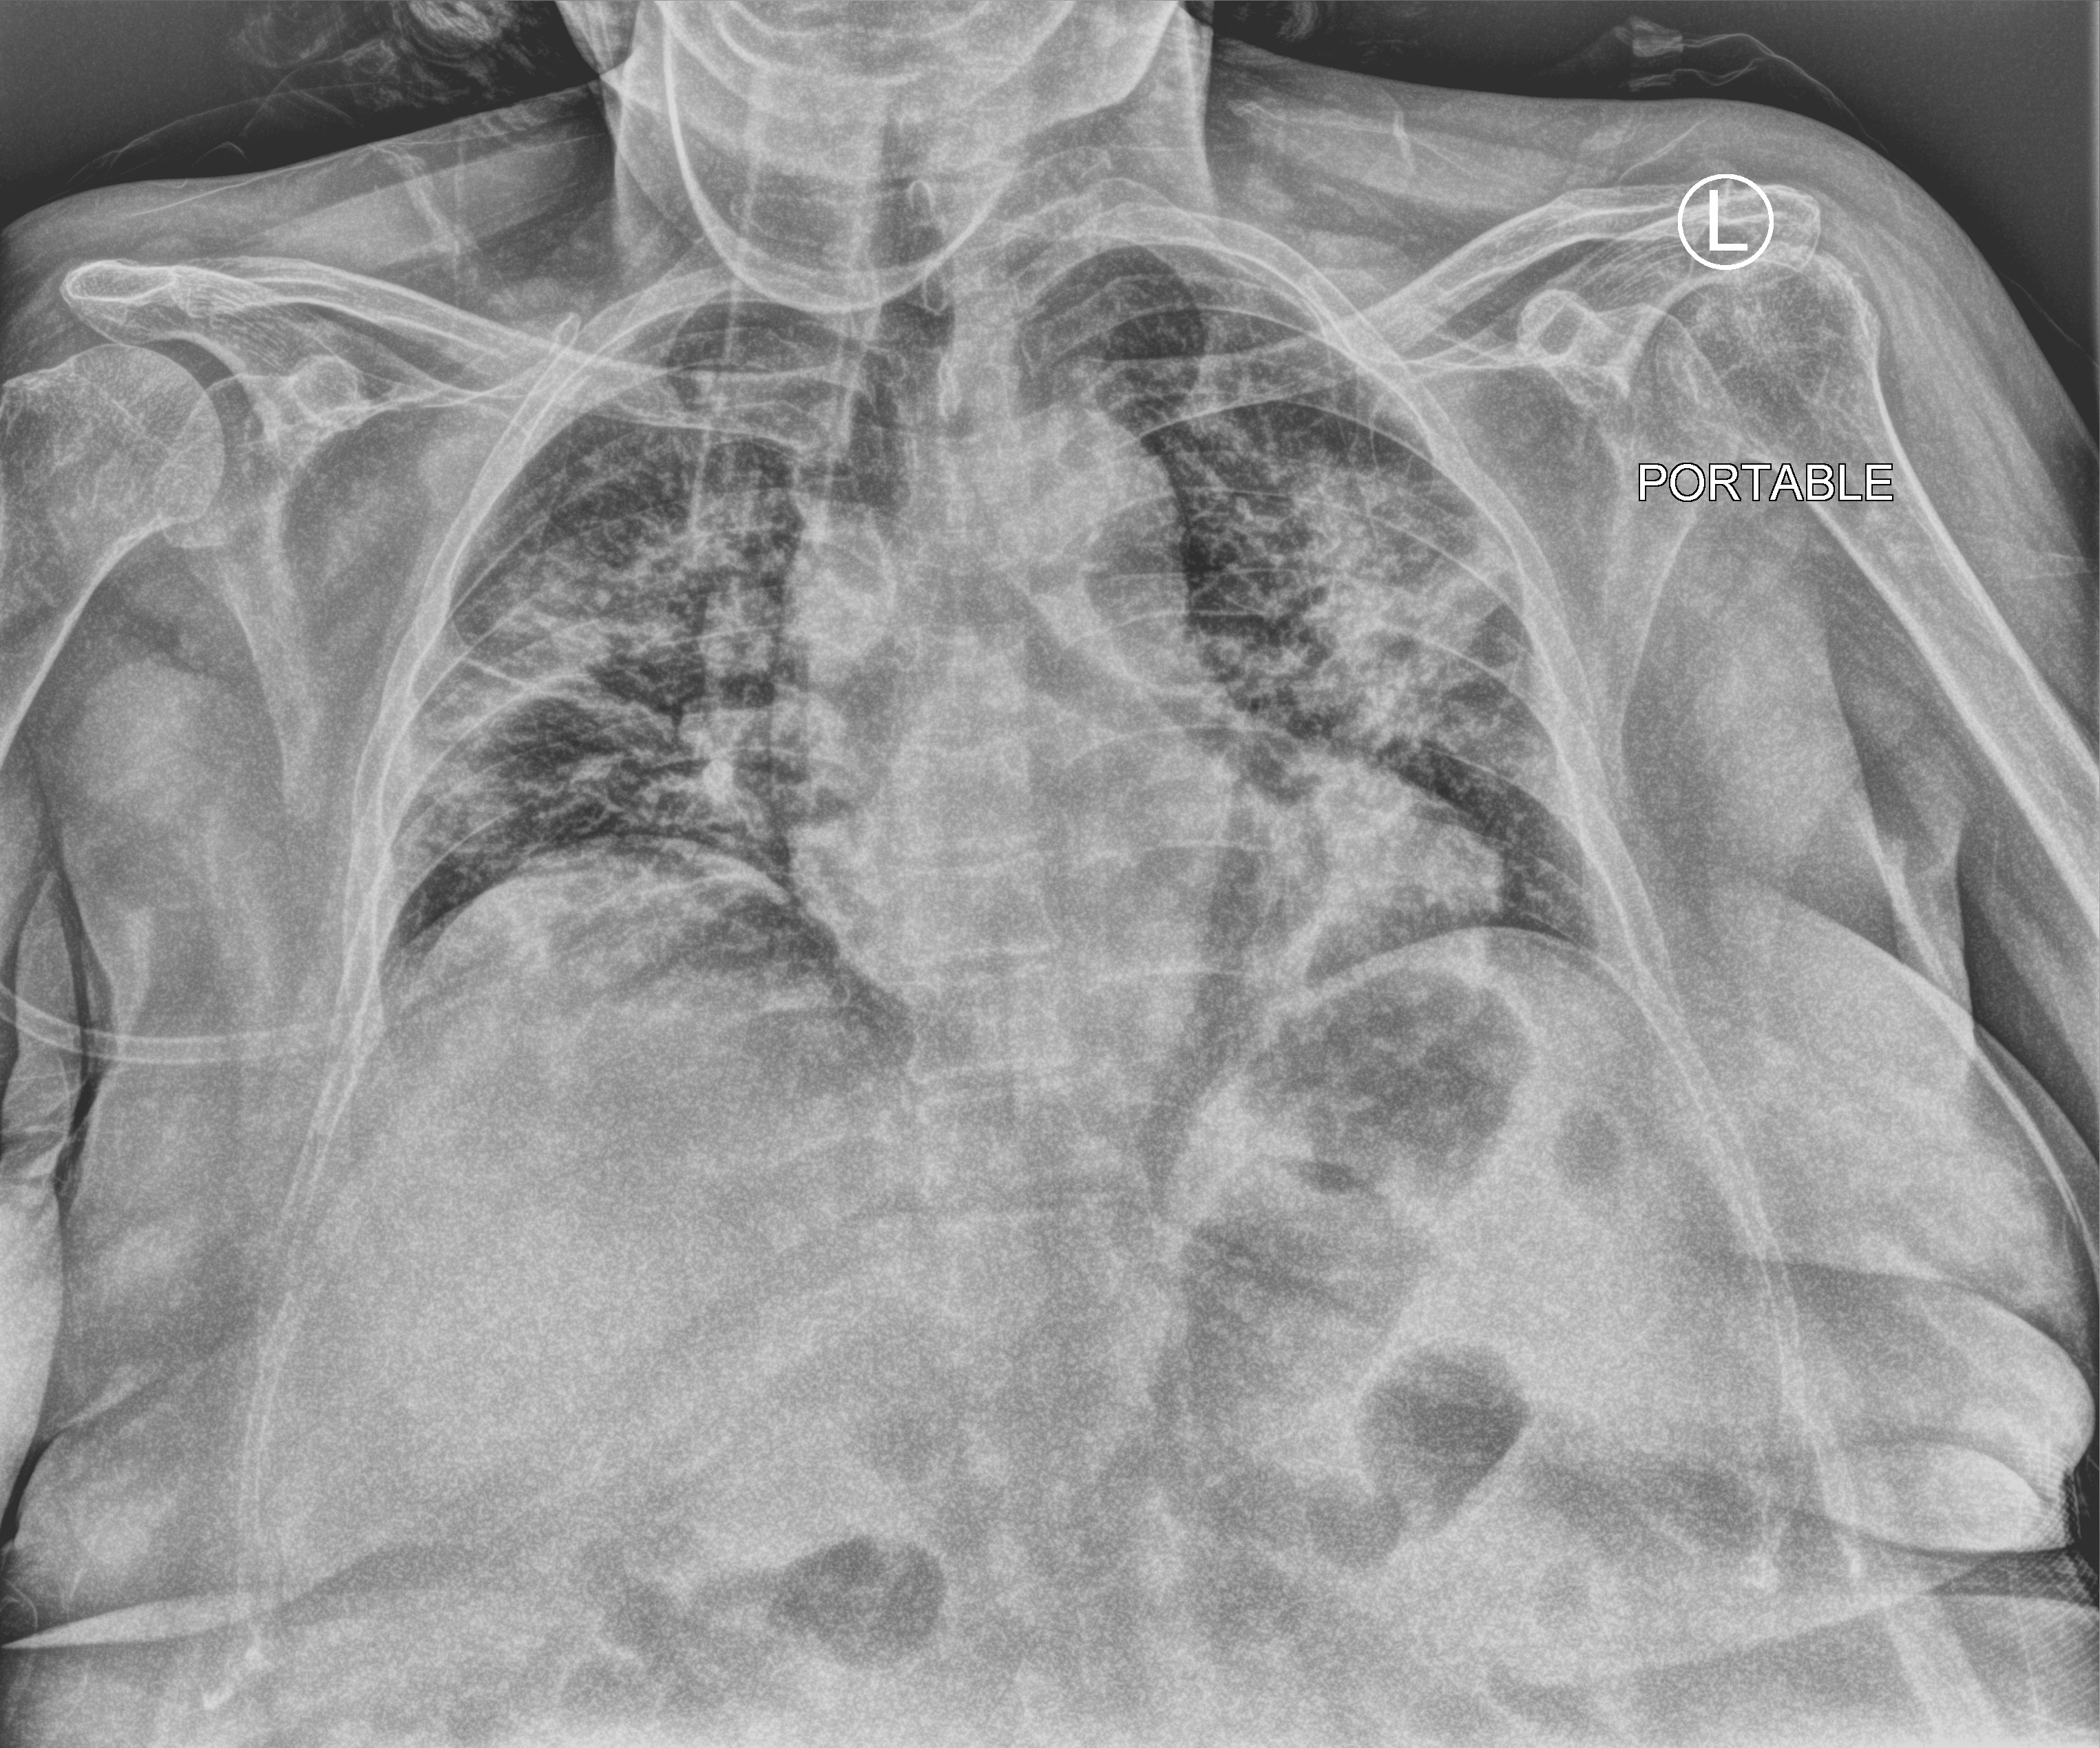
Portable chest radiograph, anteroposterior (AP) projection. Patient hospitalised with COVID-19; female, aged 60–74 years.
Admission-level facts for this patient (not findings on this image; timing relative to this image not recorded):
- admitted to intensive care during this hospital stay: yes